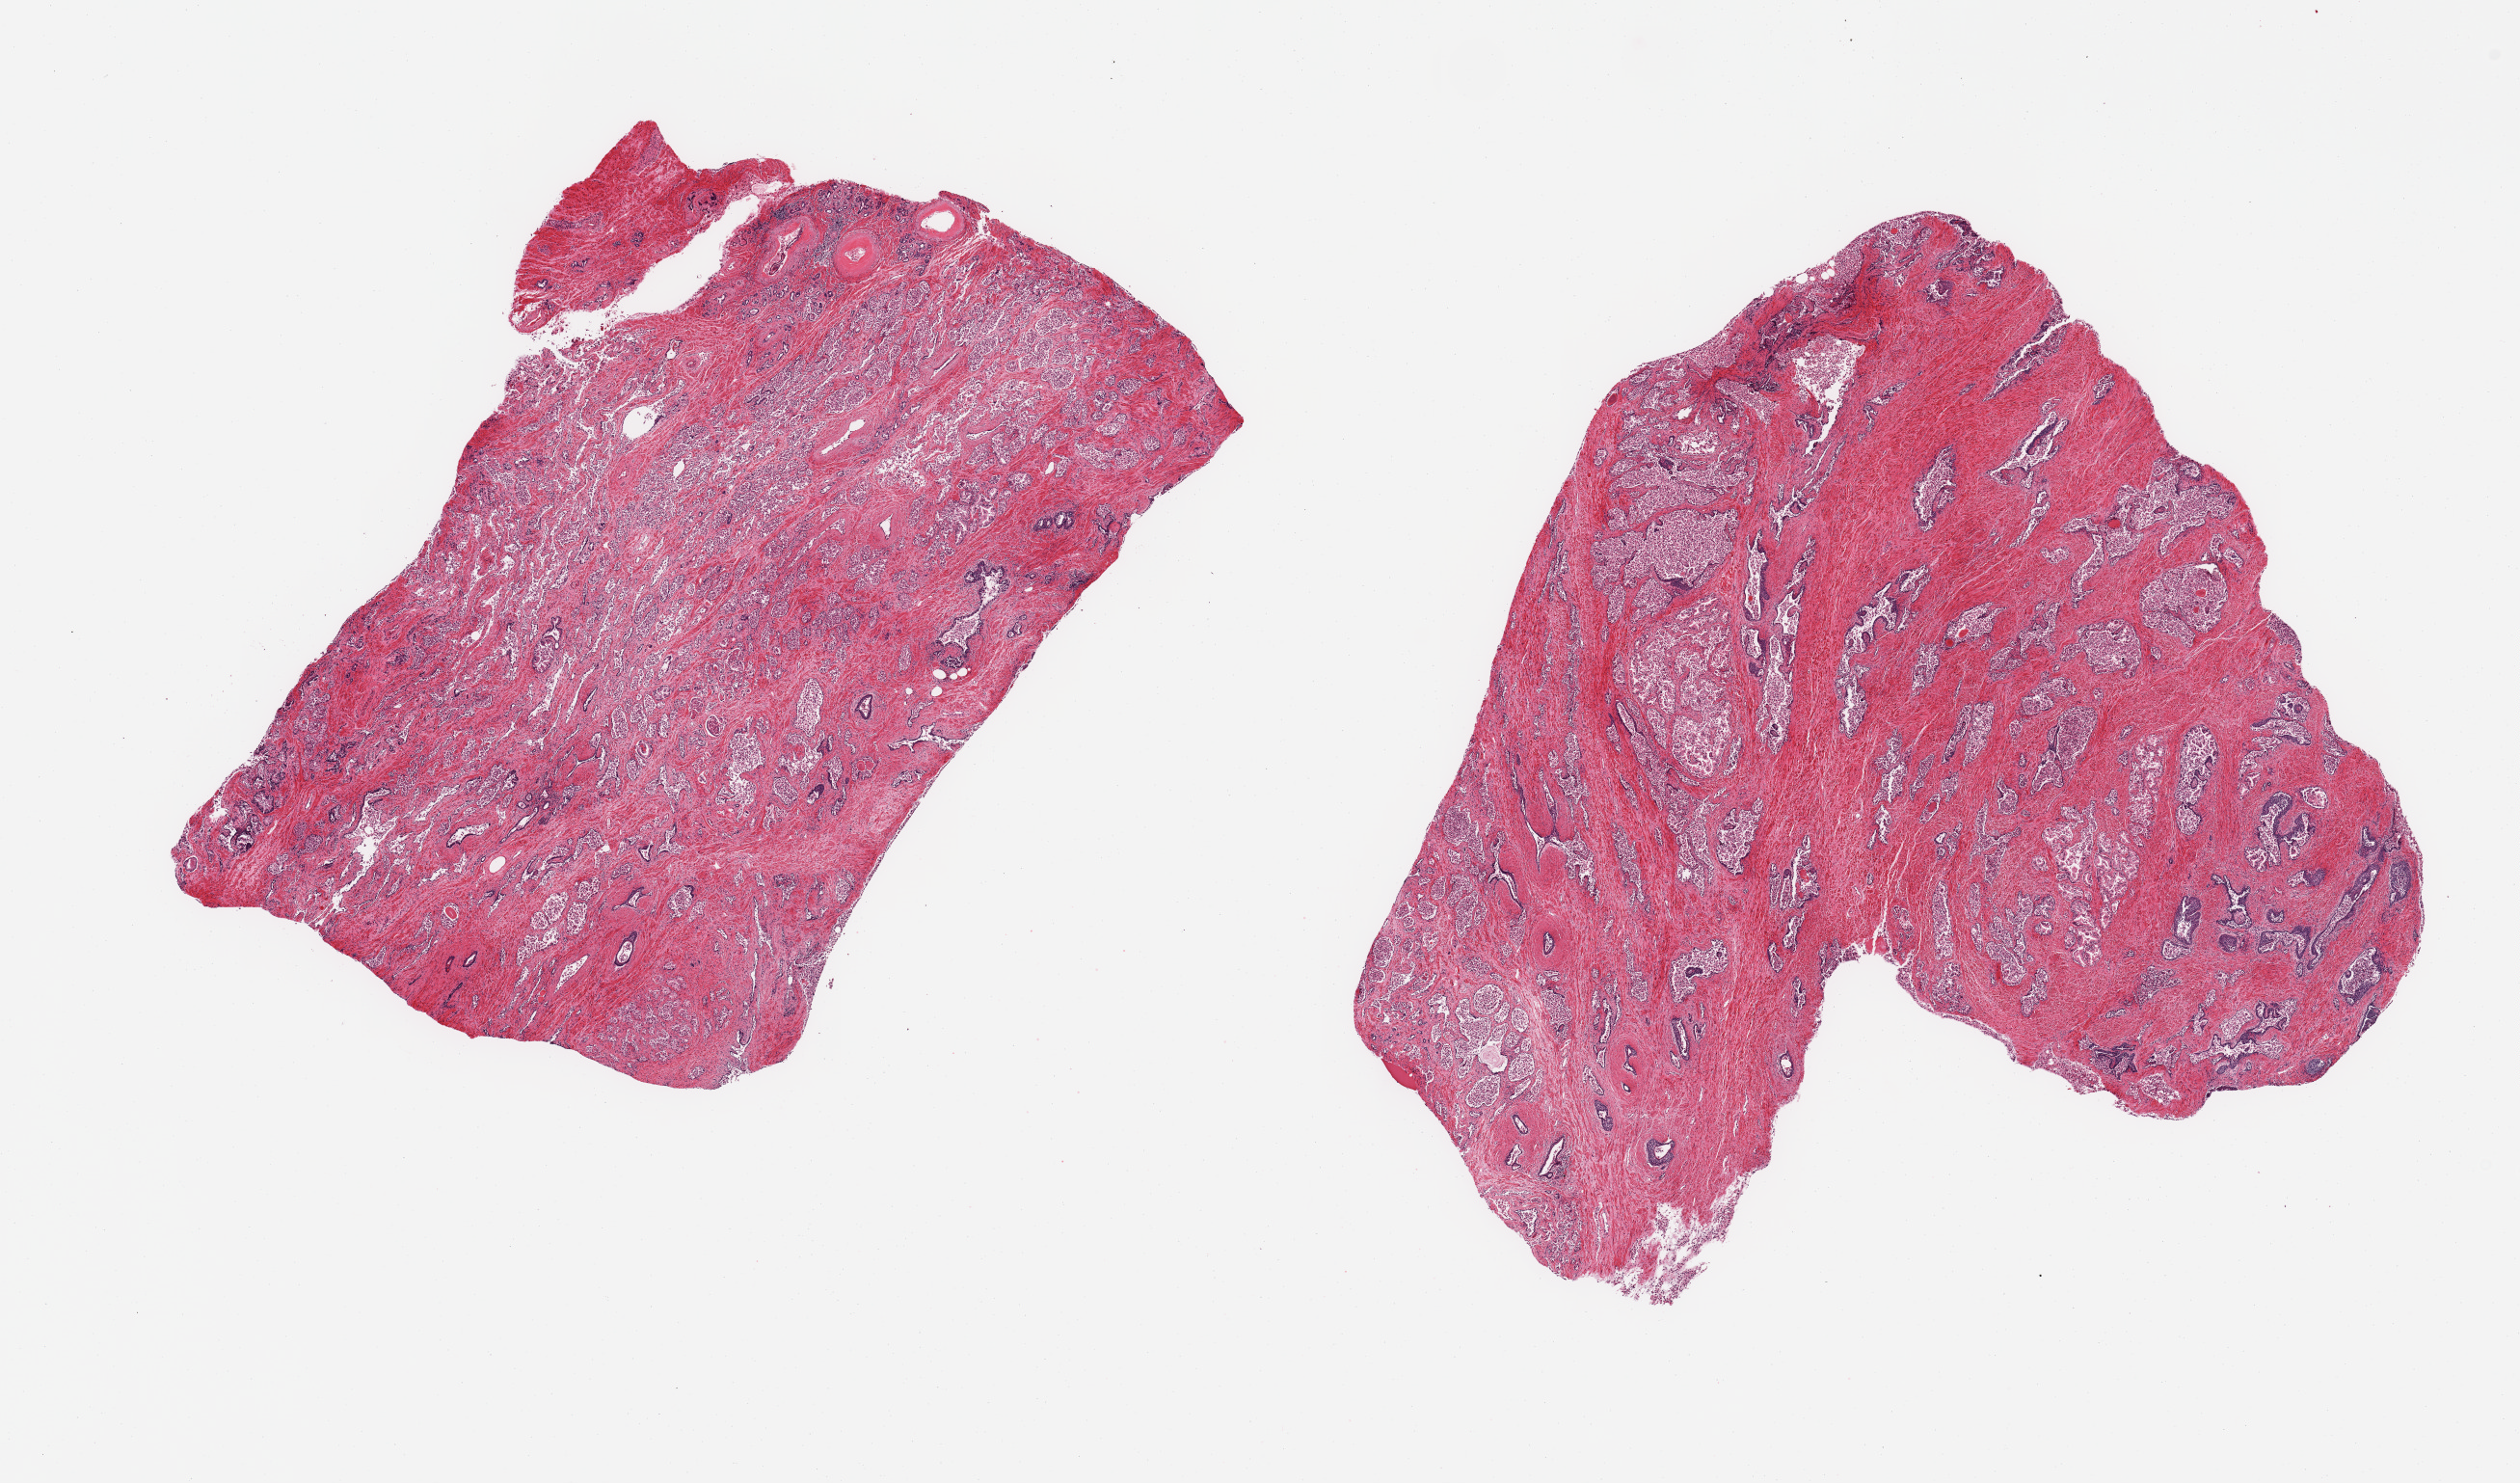
Digitized hematoxylin and eosin (H&E)-stained section — low-resolution overview of the scanned area, about 20.7 x 12.2 mm, PAXgene-fixed, paraffin-embedded tissue, section of prostate (target tissue), donor tissue sample.
Pathologist's review note for this sample: 2 pieces, glandular elements with advanced autolysis.